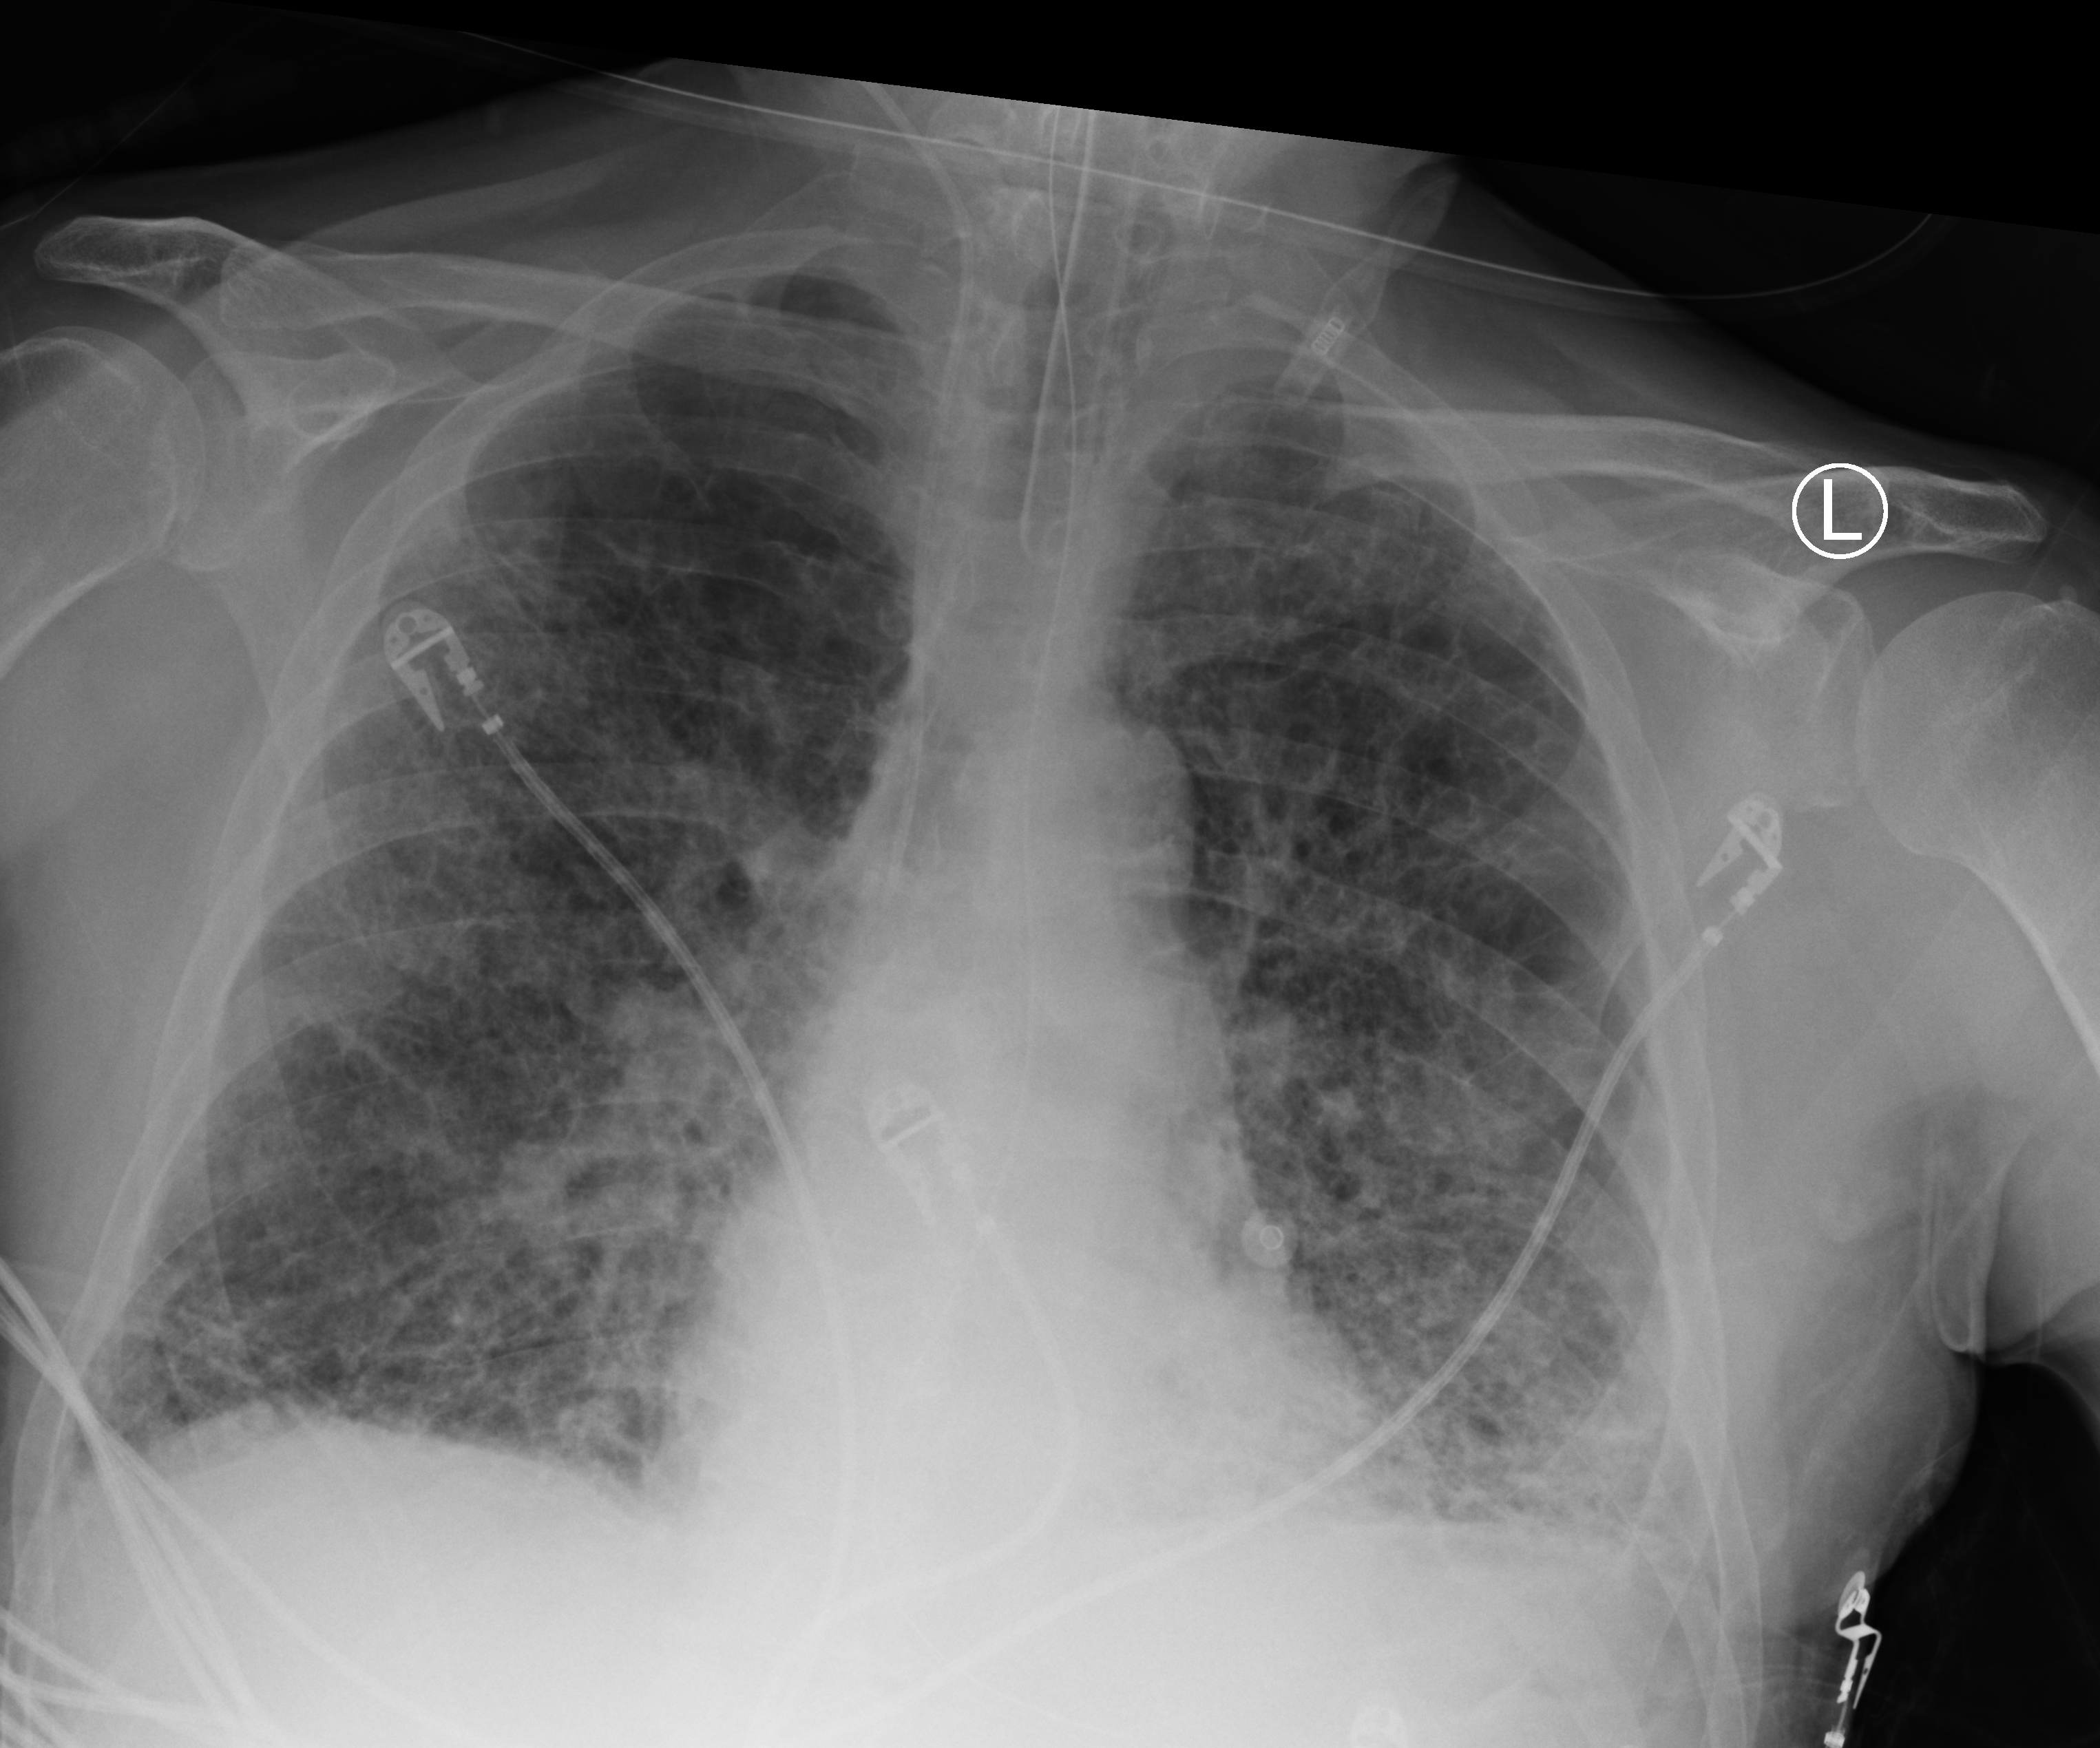
Portable chest radiograph, anteroposterior (AP) projection. Male patient hospitalised with COVID-19, age 75–90 years.
From the hospital-stay record, not from the radiograph (when in the stay this image was taken is not recorded): COPD (admission record): no.